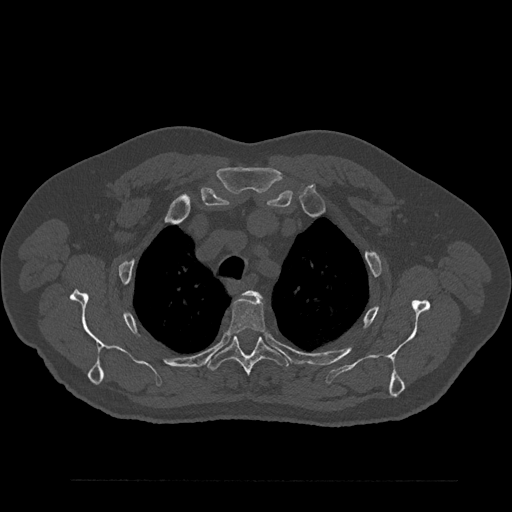
CT including the spine, one axial slice; slice 664 of 797 in the series (ordered by position); reconstruction kernel Br40s/3; bone window (W 1800 / L 400 HU); 512 × 512 image matrix, field of view 430 × 430 mm. Male patient, age 61 years. Case-level facts recorded for this patient, not image findings: primary cancer: prostate.
Structures marked on this image (semi-automatically segmented with operator editing):
- T2 vertebra: bounding box (x1, y1, x2, y2) in pixels: (245, 291, 261, 298)
- T3 vertebra: (227, 297, 266, 335)
- T4 vertebra: (207, 335, 289, 376)